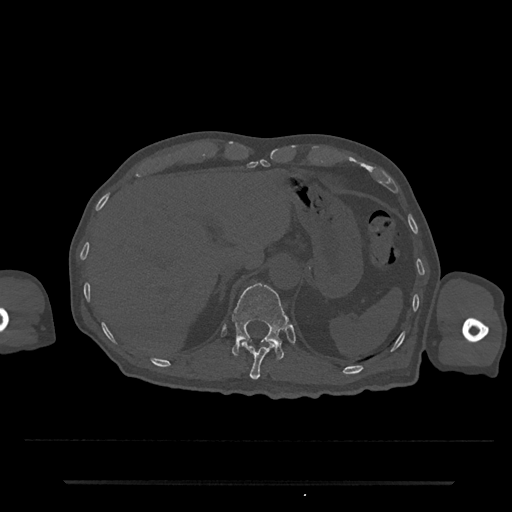
CT including the spine, one axial slice; slice 221 of 797 in the series (ordered by position); reconstruction kernel Br40s/3; bone window (W 1800 / L 400 HU); 512 × 512 image matrix, field of view 427 × 427 mm. Male patient, age 74 years. From the clinical record (not read from this slice): primary cancer: prostate.
Outlined on this slice (semi-automatic segmentation, software-assisted and operator-edited):
- T11 vertebra: bounding box <240,340,276,380> (left, top, right, bottom; pixels)
- T12 vertebra: <232,283,289,359>